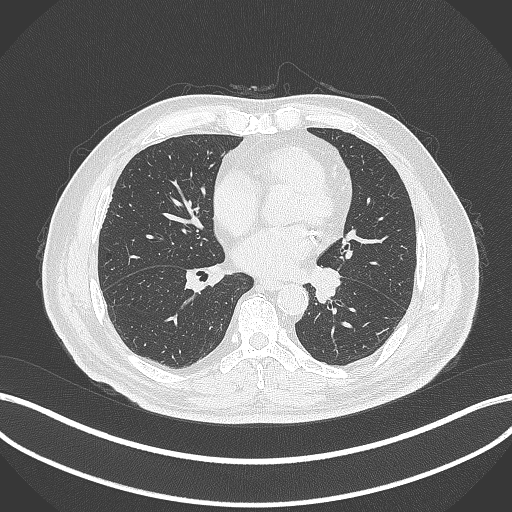
Chest CT, one axial slice. Reconstruction kernel B70f. 120 kVp. Lung window (W 1500 / L -600 HU). 1 mm slice thickness. 512 × 512 image matrix, field of view 400 × 400 mm. Male patient, age 71 years. From the clinical record (not read from this slice): clinical TNM (as recorded): T1b N0 M0.
Outlined on this slice (rectangle marked by the reading radiologist):
- lung tumour (recorded histology: squamous cell carcinoma): bounding box <307,265,343,304> (left, top, right, bottom; pixels)